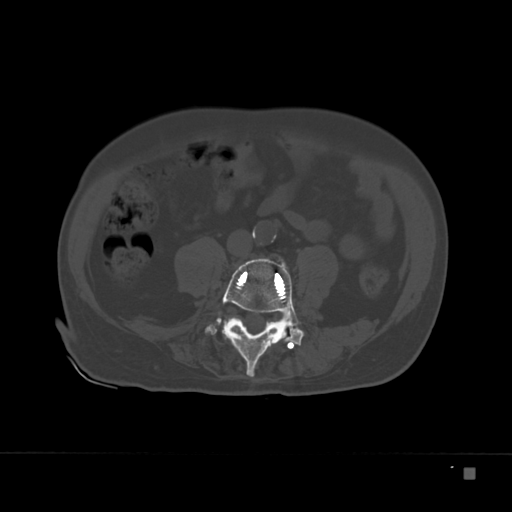
CT including the spine, one axial slice. Position 43 of 332 along the scan axis. Reconstruction kernel Br40s. 120 kVp. Bone window (W 1800 / L 400 HU). 1.5 mm slice thickness. 512 × 512 image matrix, field of view 389 × 389 mm. Male patient, age 72 years. From the clinical record (not read from this slice): primary cancer: skeletal.
Outlined on this slice (semi-automatic segmentation, software-assisted and operator-edited):
- L4 vertebra: box from (x=205, y=258) to (x=304, y=377) px